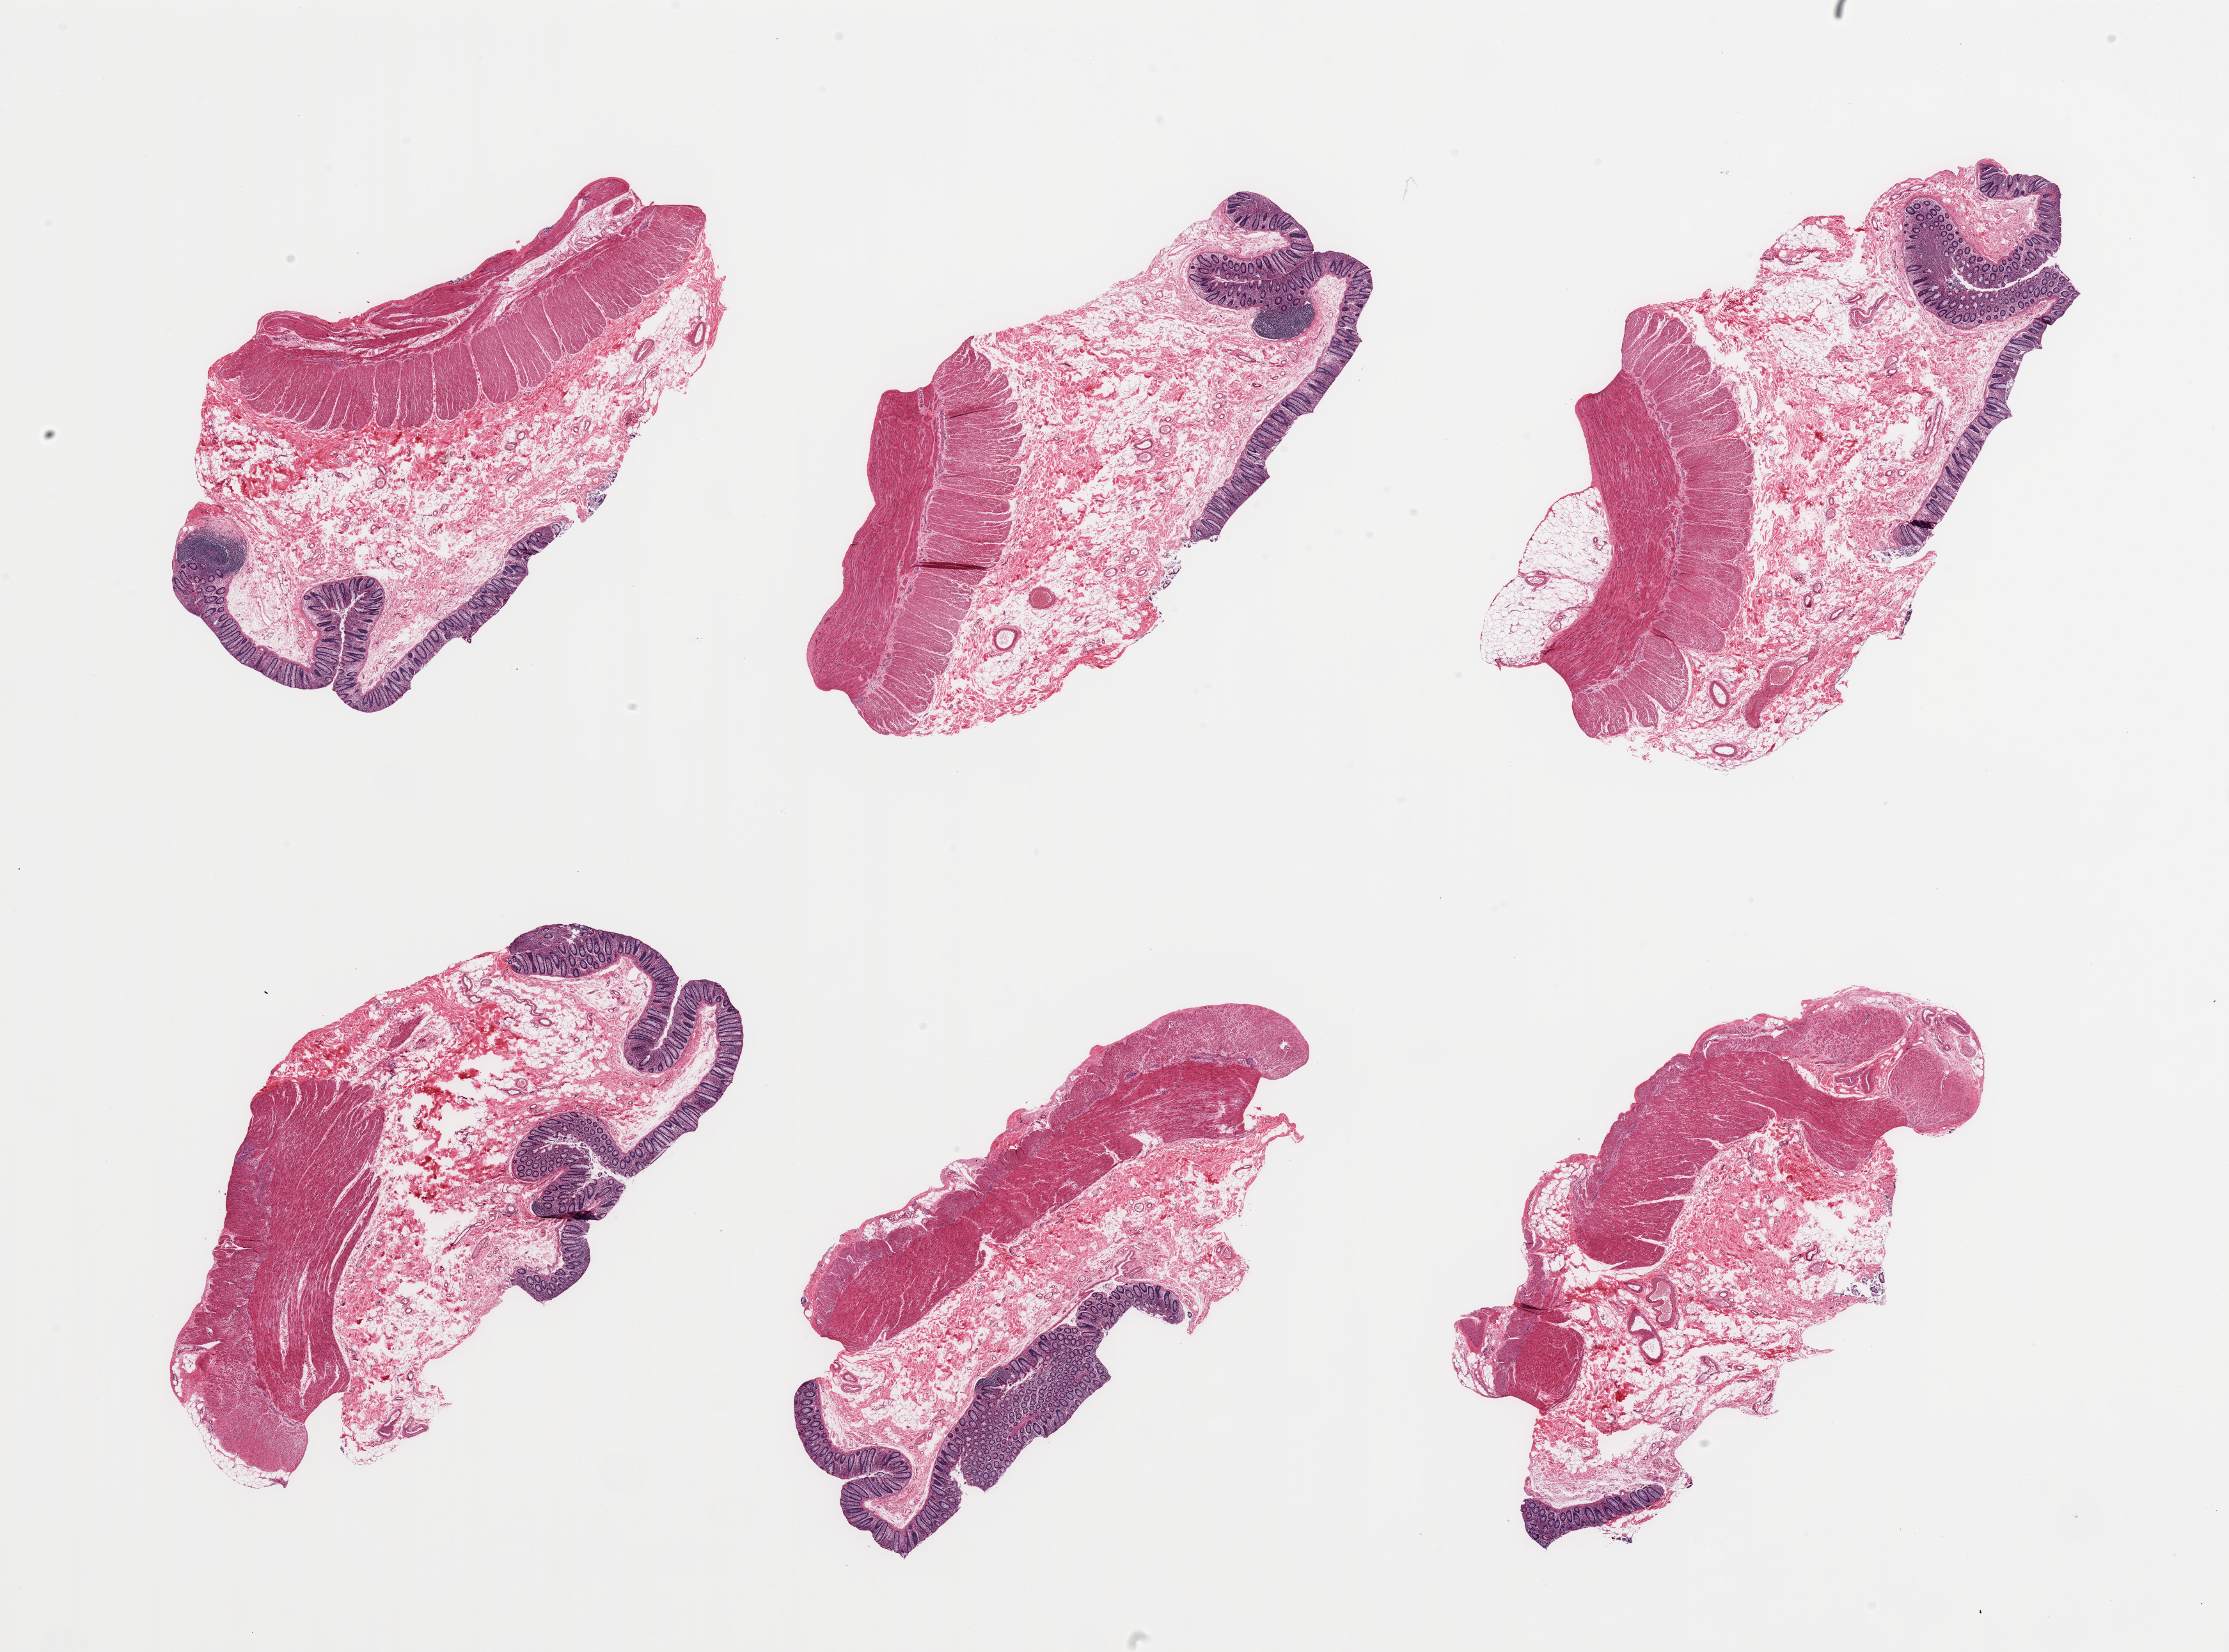
Whole-slide image, hematoxylin and eosin (H&E) stain — shown as a low-resolution overview of the whole scanned area (about 27.6 x 20.4 mm, from a 20x scan). PAXgene-fixed, paraffin-embedded tissue. Sampled site (target tissue): transverse colon. Donor tissue sample. Male donor.
Reviewer comment on this tissue sample: 6 pieces; focal moderate autolysis.